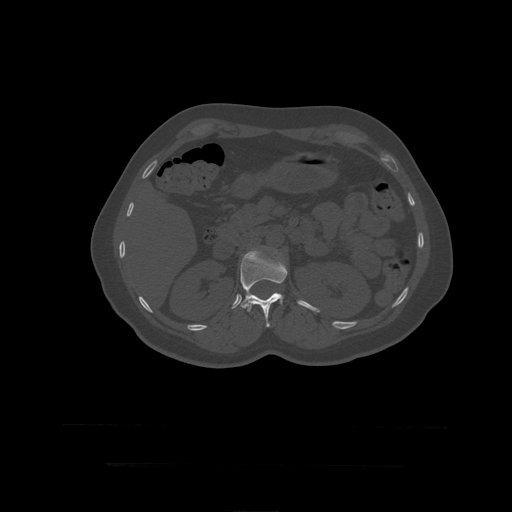
CT including the spine, one axial slice. Position 171 of 399 along the scan axis. Reconstruction kernel STANDARD. Bone window (W 1800 / L 400 HU). 1.25 mm slice thickness. 512 × 512 image matrix, field of view 450 × 450 mm. Patient age 41 years. From the clinical record (not read from this slice): primary cancer: breast.
Outlined on this slice (semi-automatically segmented with operator editing):
- L1 vertebra: bounding box [x1, y1, x2, y2] px = [241, 251, 288, 328]